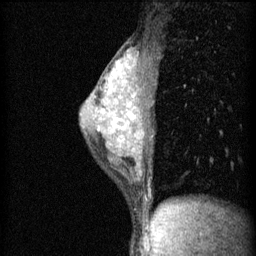
Breast MRI (dynamic contrast-enhanced), one sagittal slice. Position 38 of 60 along the scan axis. 3 images stored at this slice position (order not interpretable as contrast timing). 1.5 T. TE 4.2 ms, TR 11 ms. 2 mm slice thickness. 256 × 256 image matrix, field of view 180 × 180 mm. Female patient, age 40 years.
Annotated regions visible in this slice (semi-automatic segmentation, software-assisted and operator-edited):
- analysis volume of interest (the breast-tissue region the enhancement analysis was run in; not a lesion): bounding box <80,50,153,183> (left, top, right, bottom; pixels)
- tumour enhancement mask (voxels above the 70 % enhancement threshold inside the analysis volume of interest): <113,104,135,129>